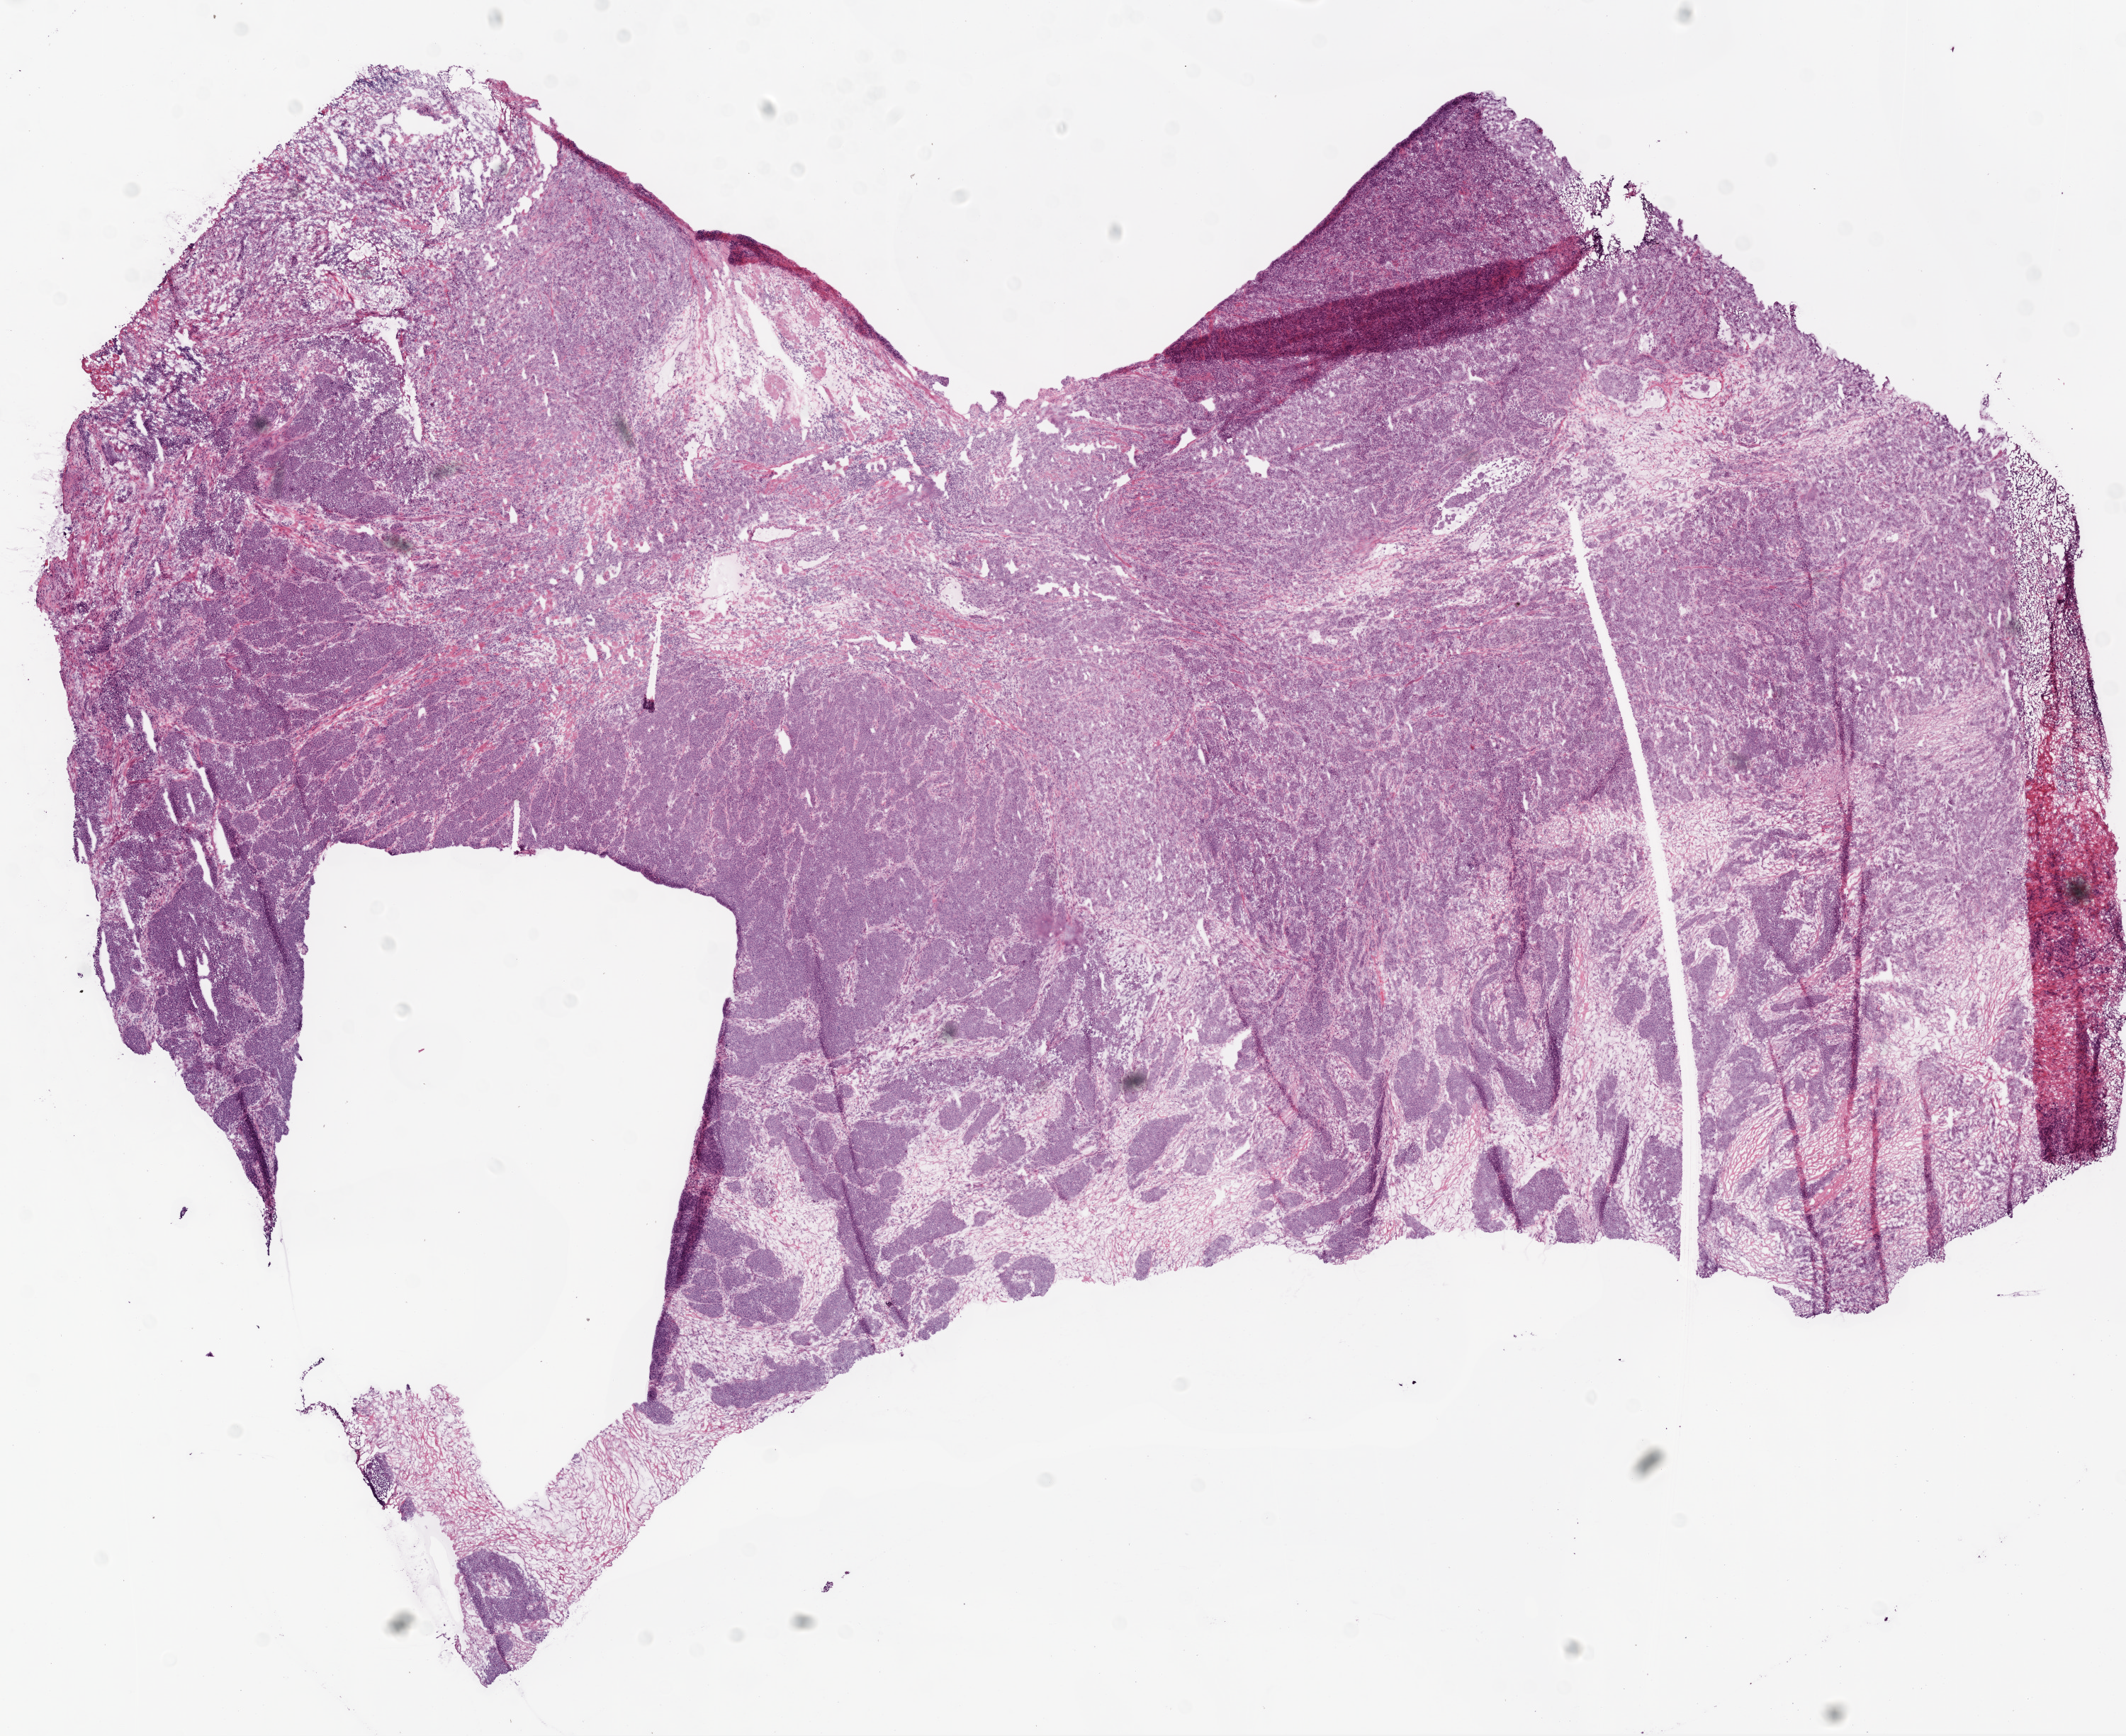
Whole-slide histology image, H&E, a low-resolution overview of the entire scanned area, about 12.0 x 9.8 mm (slide scanned at 20x). Frozen section from the bottom of the tissue portion. Primary tumour sample from the ovary. Female patient; age at initial diagnosis 71 years. Histologic grade: G3 (poorly differentiated). Composition of this section per pathologist review: tumour cells 98%, tumour nuclei 90%, normal cells 0%, stromal cells 0%, necrosis 2%. Infiltration values recorded for this section: lymphocyte infiltration 5%.
Laterality: right. Pathologic diagnosis: Serous cystadenocarcinoma, NOS. FIGO stage: IIIC.